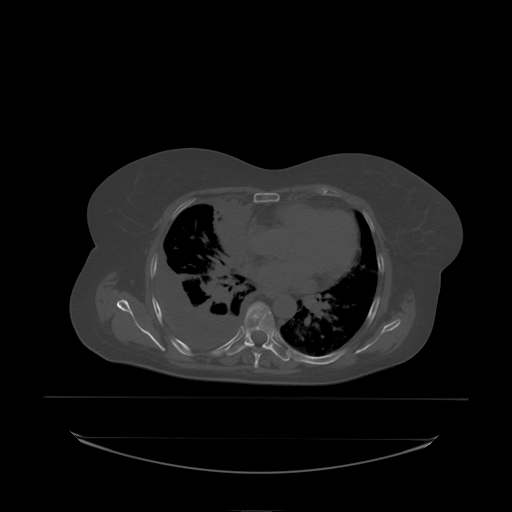
CT including the spine, one axial slice. Position 145 of 242 along the scan axis. Bone window (W 1800 / L 400 HU). 512 × 512 image matrix, field of view 500 × 500 mm. Female patient, age 53 years. From the clinical record (not read from this slice): primary cancer: lung; vertebrae with lytic lesions (as recorded): T7, L1.
Structures marked on this image (semi-automatic segmentation, software-assisted and operator-edited):
- T6 vertebra: box from (x=246, y=308) to (x=254, y=331) px
- T7 vertebra: (x=245, y=303)–(x=276, y=338)